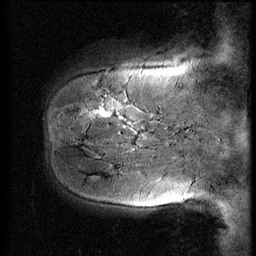
Breast MRI (dynamic contrast-enhanced), one sagittal slice; slice 10 of 56 in the series (ordered by position); 3 images stored at this slice position (order not interpretable as contrast timing); 1.5 T; TE 4.2 ms, TR 9 ms; 2.5 mm slice thickness; 256 × 256 image matrix, field of view 180 × 180 mm. Female patient, age 51 years. Case-level facts recorded for this patient, not image findings: setting: breast cancer imaged before/during neoadjuvant chemotherapy; receptor status: HR-positive, HER2-negative.
Annotated regions visible in this slice (semi-automatically segmented with operator editing):
- analysis volume of interest (the breast-tissue region the enhancement analysis was run in; not a lesion): bounding box [x1, y1, x2, y2] px = [44, 58, 167, 161]
- tumour enhancement mask (voxels above the 140 % enhancement threshold inside the analysis volume of interest): [90, 106, 131, 125]